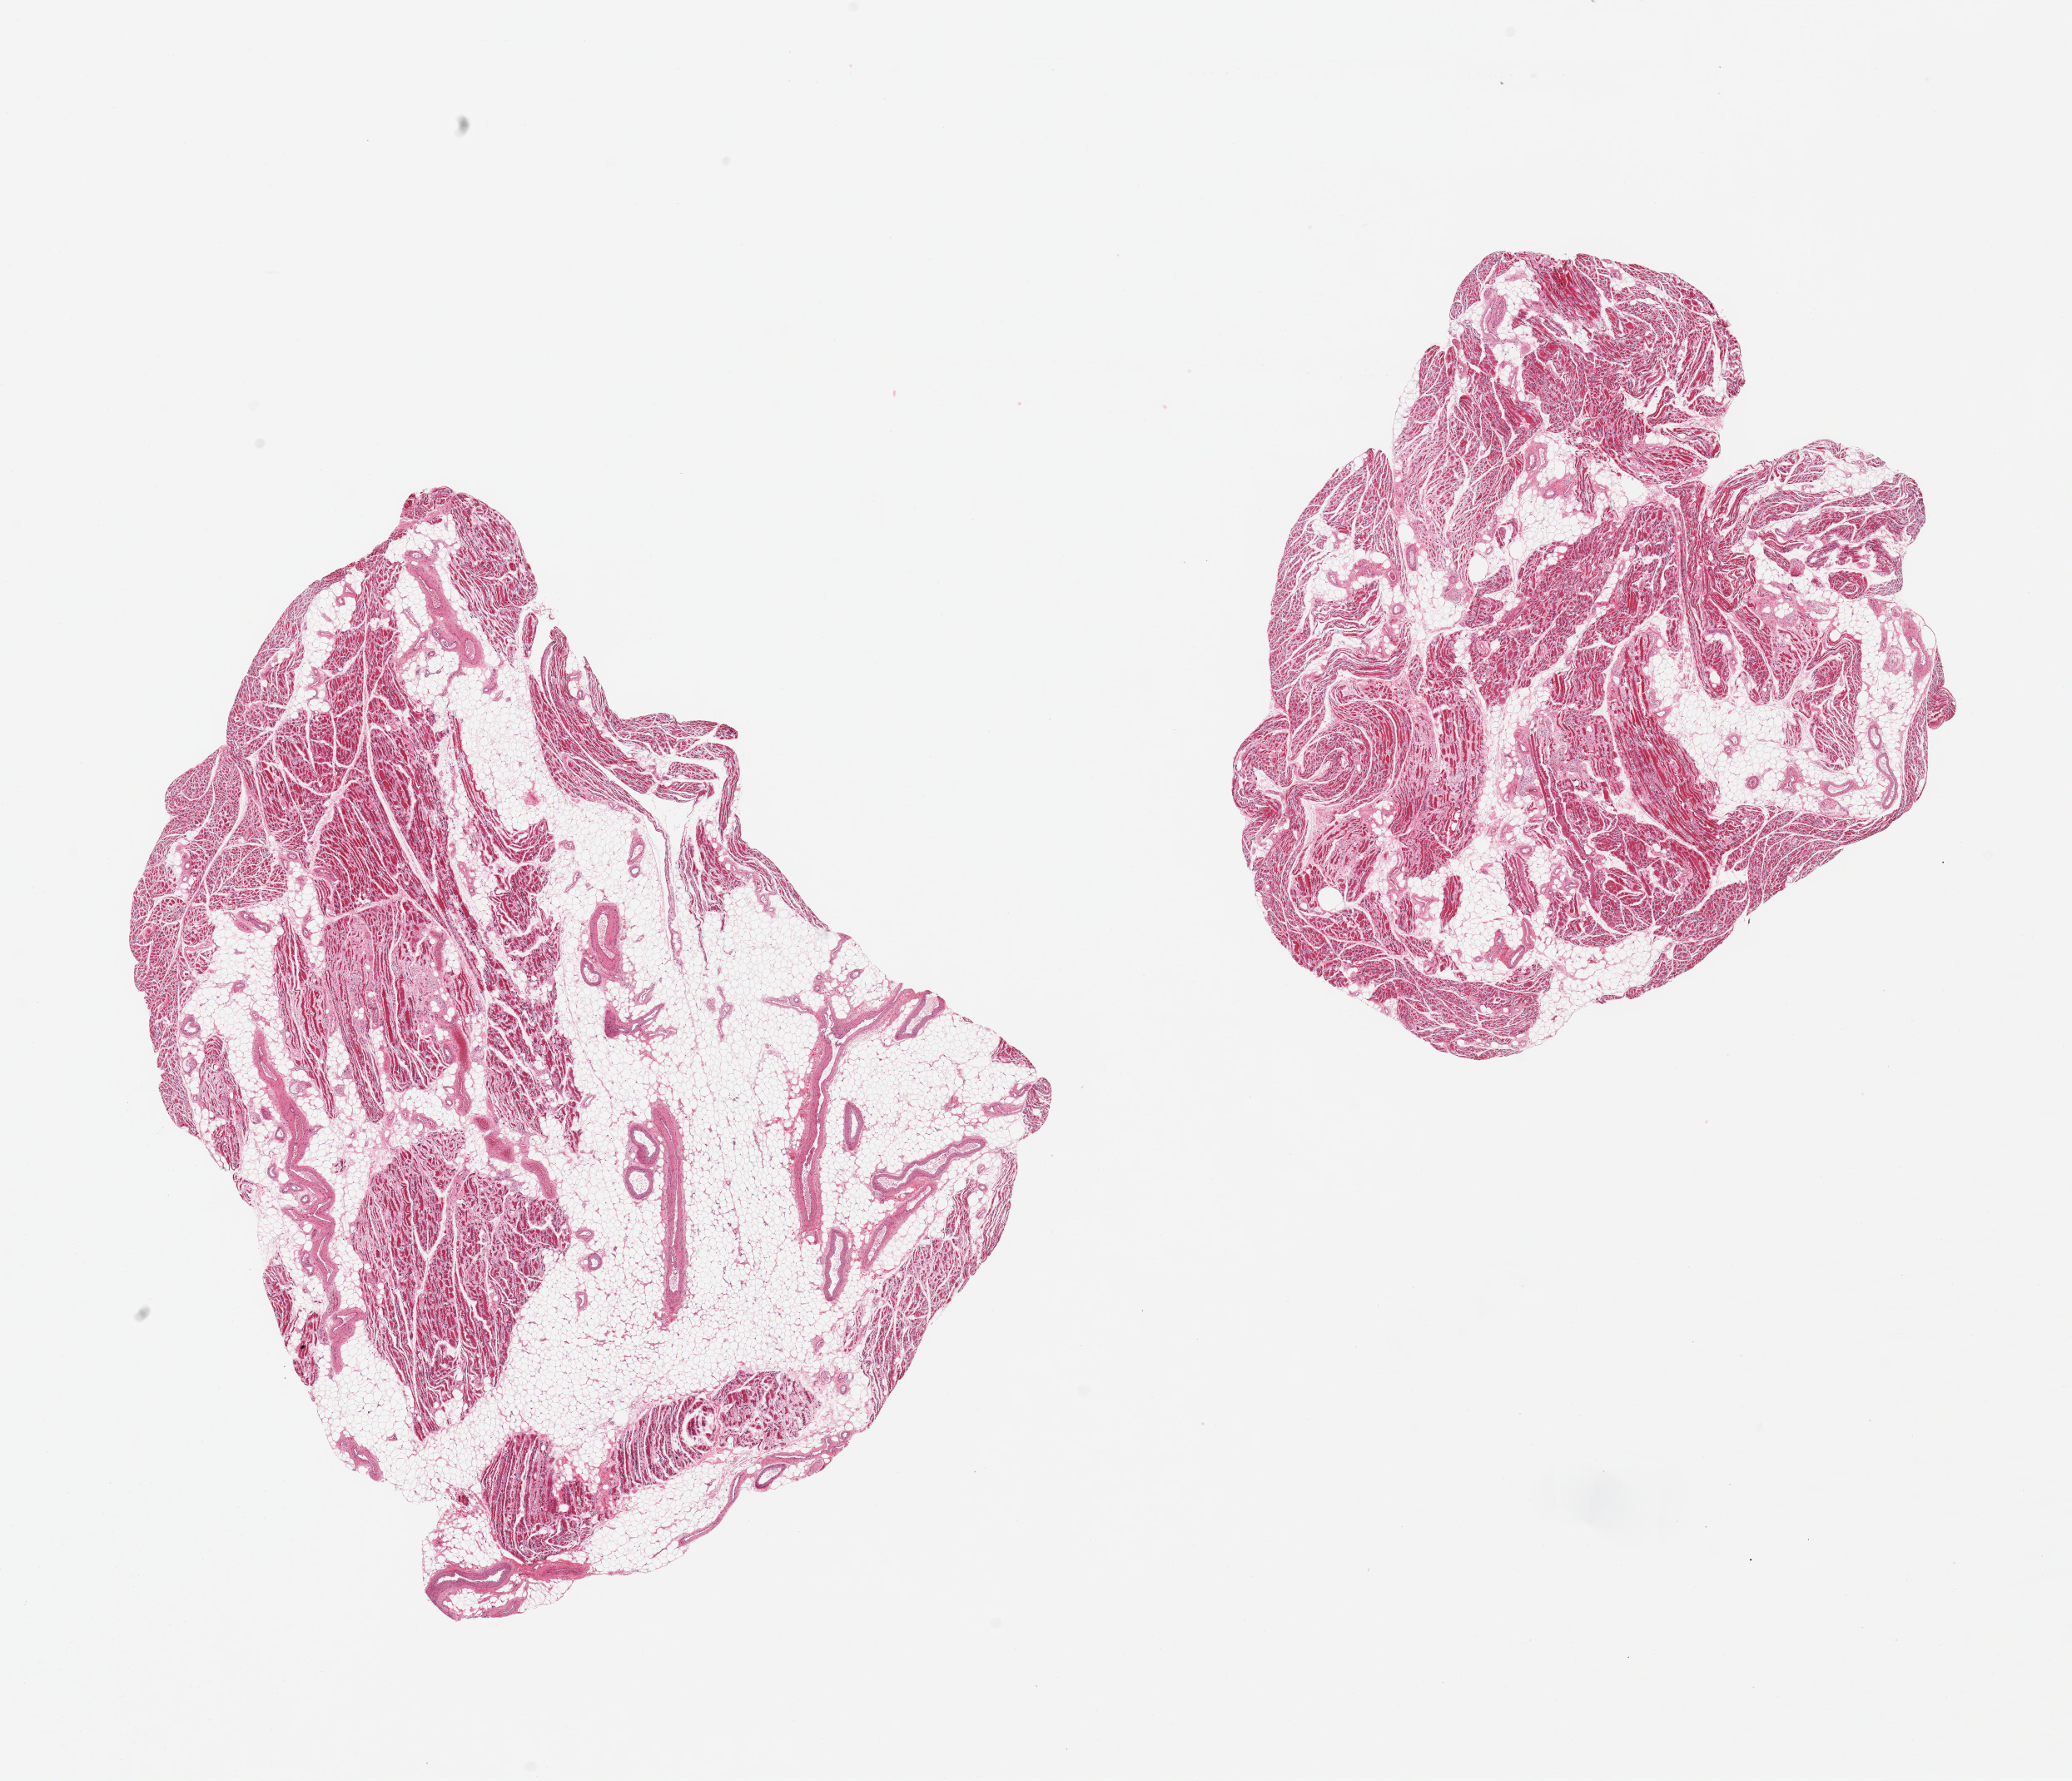
H&E whole-slide image, brightfield, low-resolution overview of the scanned area, about 19.7 x 16.9 mm, PAXgene-fixed, paraffin-embedded tissue, sampled site (target tissue): skeletal muscle, tissue donor sample. Donor sex: female.
Pathologist's review note for this sample: 2 pieces; marked atrophy with fibrous replacement & 60% and 30% internal fat (consistent with paraplegia).